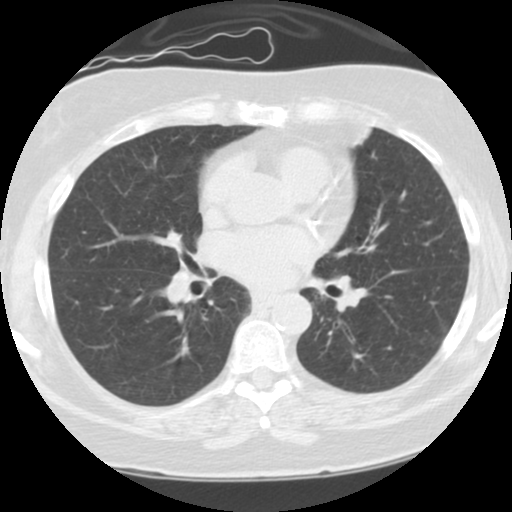
Low-dose screening chest CT, one axial slice. Slice 57 of 108 in the series (ordered by position). Reconstruction kernel STANDARD. 120 kVp. Lung window (W 1500 / L -600 HU). 2.5 mm slice thickness. 512 × 512 image matrix, field of view 300 × 300 mm.
Annotated regions visible in this slice (expert manual segmentation):
- lesion 1 (tumor, hilum of left lung): bounding box <331,276,367,310> (left, top, right, bottom; pixels)